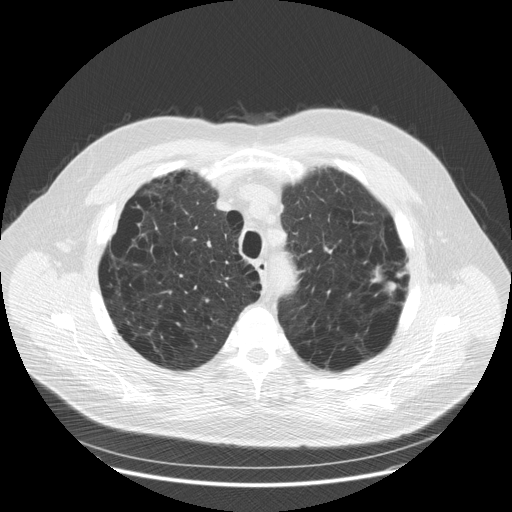
Low-dose screening chest CT, axial slice. Baseline annual screen. Lung window (W 1500 / L -600 HU). 2.5 mm slice thickness. Standard (soft-tissue) reconstruction kernel (STANDARD). Male participant, aged 70 years at enrolment. Current smoker at enrolment.
- Expert-annotated lung lesion, box from (x=362, y=251) to (x=414, y=301) px.
- Reader record for this screening exam (exam-level; its link to the box is not recorded): non-calcified nodule or mass ≥4 mm, left upper lobe, 25 × 13 mm, spiculated (stellate) margins, soft tissue attenuation.
- Official screen result: positive, change unspecified: nodule(s) >= 4 mm or enlarging nodule(s), mass(es), or other non-specific abnormalities suspicious for lung cancer.
- Participant outcome: lung cancer diagnosed 62 days after this screen — adenocarcinoma, NOS, left upper lobe, moderately differentiated (G2), stage IA (AJCC 6th edition), 22 mm at pathology.